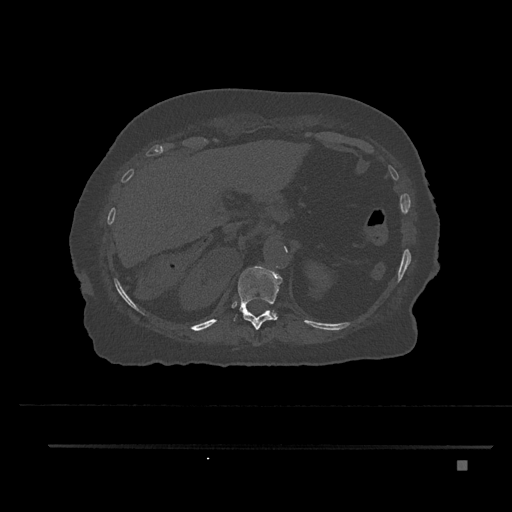
CT including the spine, one axial slice. Position 308 of 797 along the scan axis. Reconstruction kernel Br40s/3. Bone window (W 1800 / L 400 HU). 0.5 mm slice thickness. 512 × 512 image matrix, field of view 437 × 437 mm. Female patient, age 76 years. Case-level facts recorded for this patient, not image findings: primary cancer: lung; vertebrae with lytic lesions (as recorded): T11, L3.
Structures marked on this image (semi-automatically segmented with operator editing):
- T11 vertebra: bounding box <233,266,282,330> (left, top, right, bottom; pixels)